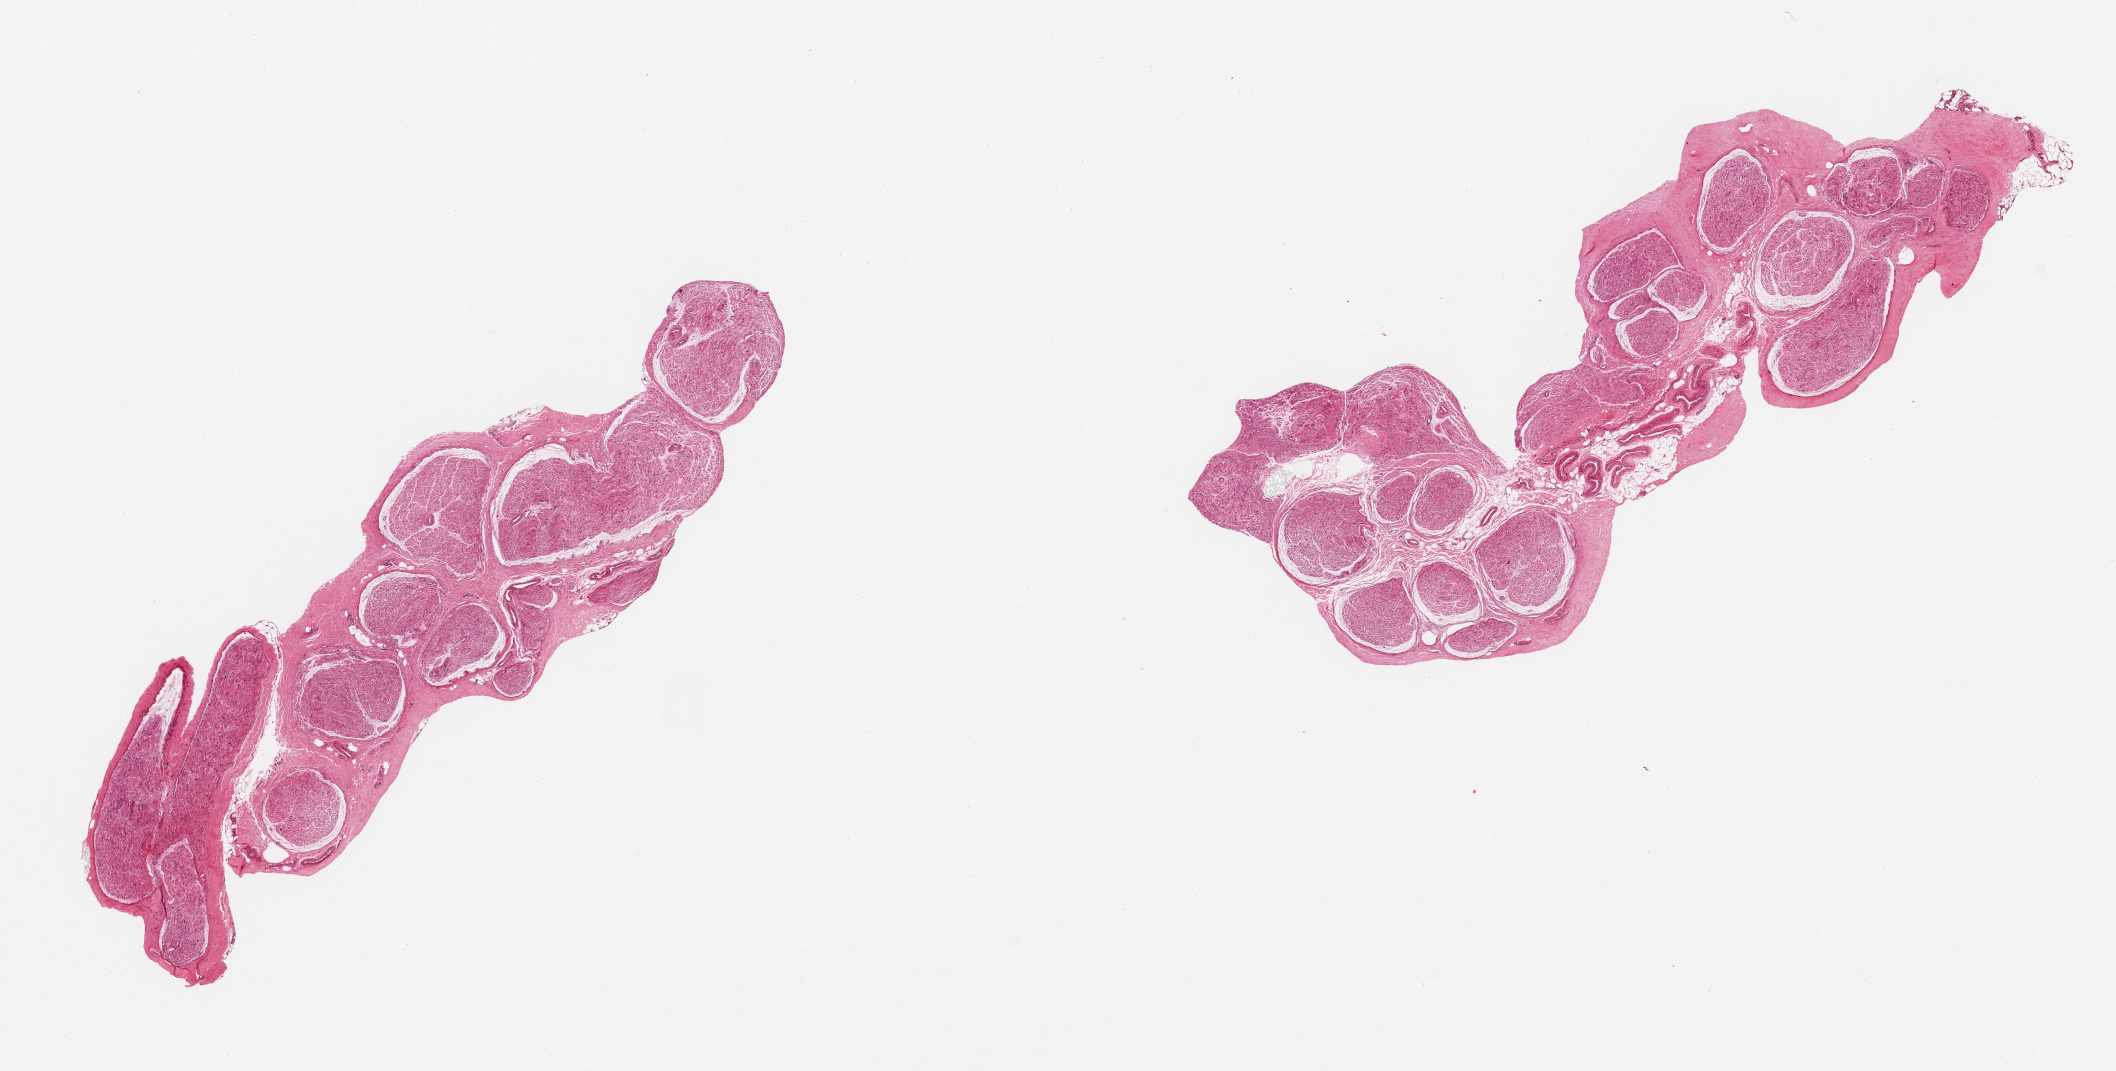
Whole-slide image, haematoxylin and eosin stain — low-resolution overview of the scanned area, about 16.7 x 8.5 mm; PAXgene-fixed, paraffin-embedded tissue; section of tibial nerve (target tissue); donor tissue sample. Donor sex: male.
* reviewer comment on this tissue sample: 2 pieces, no adherent fat, clean specimen